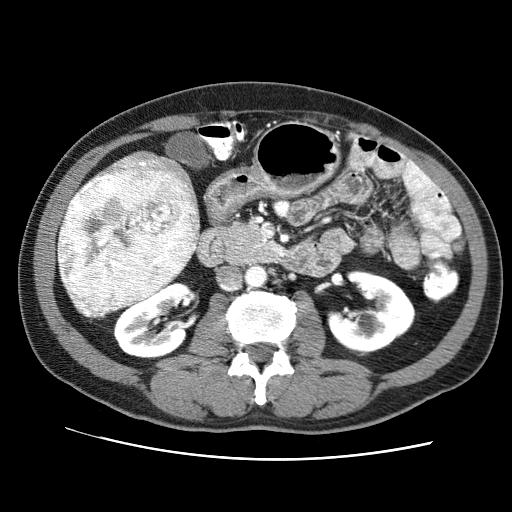
Contrast-enhanced abdominal CT (liver protocol), one axial slice; slice 25 of 71 in the series (ordered by position); reconstruction kernel STANDARD; 120 kVp; soft-tissue window (W 400 / L 40 HU); 2.5 mm slice thickness; 512 × 512 image matrix, field of view 360 × 360 mm. Case-level facts recorded for this patient, not image findings: diagnosis: hepatocellular carcinoma (patient treated with transarterial chemoembolisation; whether this scan precedes or follows treatment is not stated here); TNM stage (as recorded): Stage-II; Child-Pugh class: A; tumour nodularity: multinodular; tumour size: 4.6 cm.
Structures marked on this image (semi-automatic segmentation, software-assisted and operator-edited):
- liver parenchyma outside the tumour (the mass and vessels are separate outlines, so this box may not span the whole liver): bounding box <57,150,200,318> (left, top, right, bottom; pixels)
- mass: <57,168,199,318>
- liver vessels: <84,159,189,314>